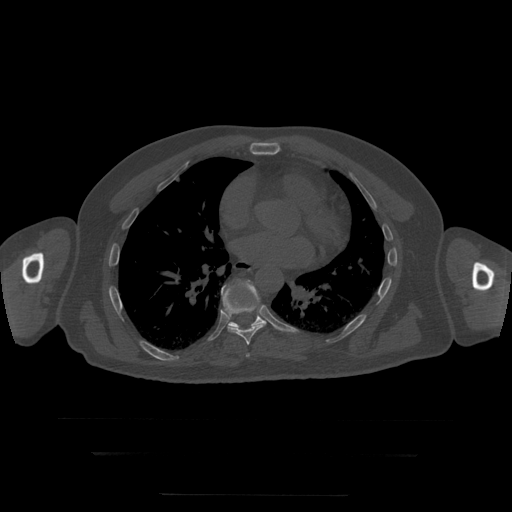
CT including the spine, one axial slice; 120 kVp; bone window (W 1800 / L 400 HU); 1.25 mm slice thickness; 512 × 512 image matrix, field of view 510 × 510 mm. Patient age 73 years. From the clinical record (not read from this slice): primary cancer: prostate.
Outlined on this slice (semi-automatic segmentation, software-assisted and operator-edited):
- T7 vertebra: bounding box <246,354,250,357> (left, top, right, bottom; pixels)
- T8 vertebra: <221,282,267,346>
- T9 vertebra: <228,281,266,329>